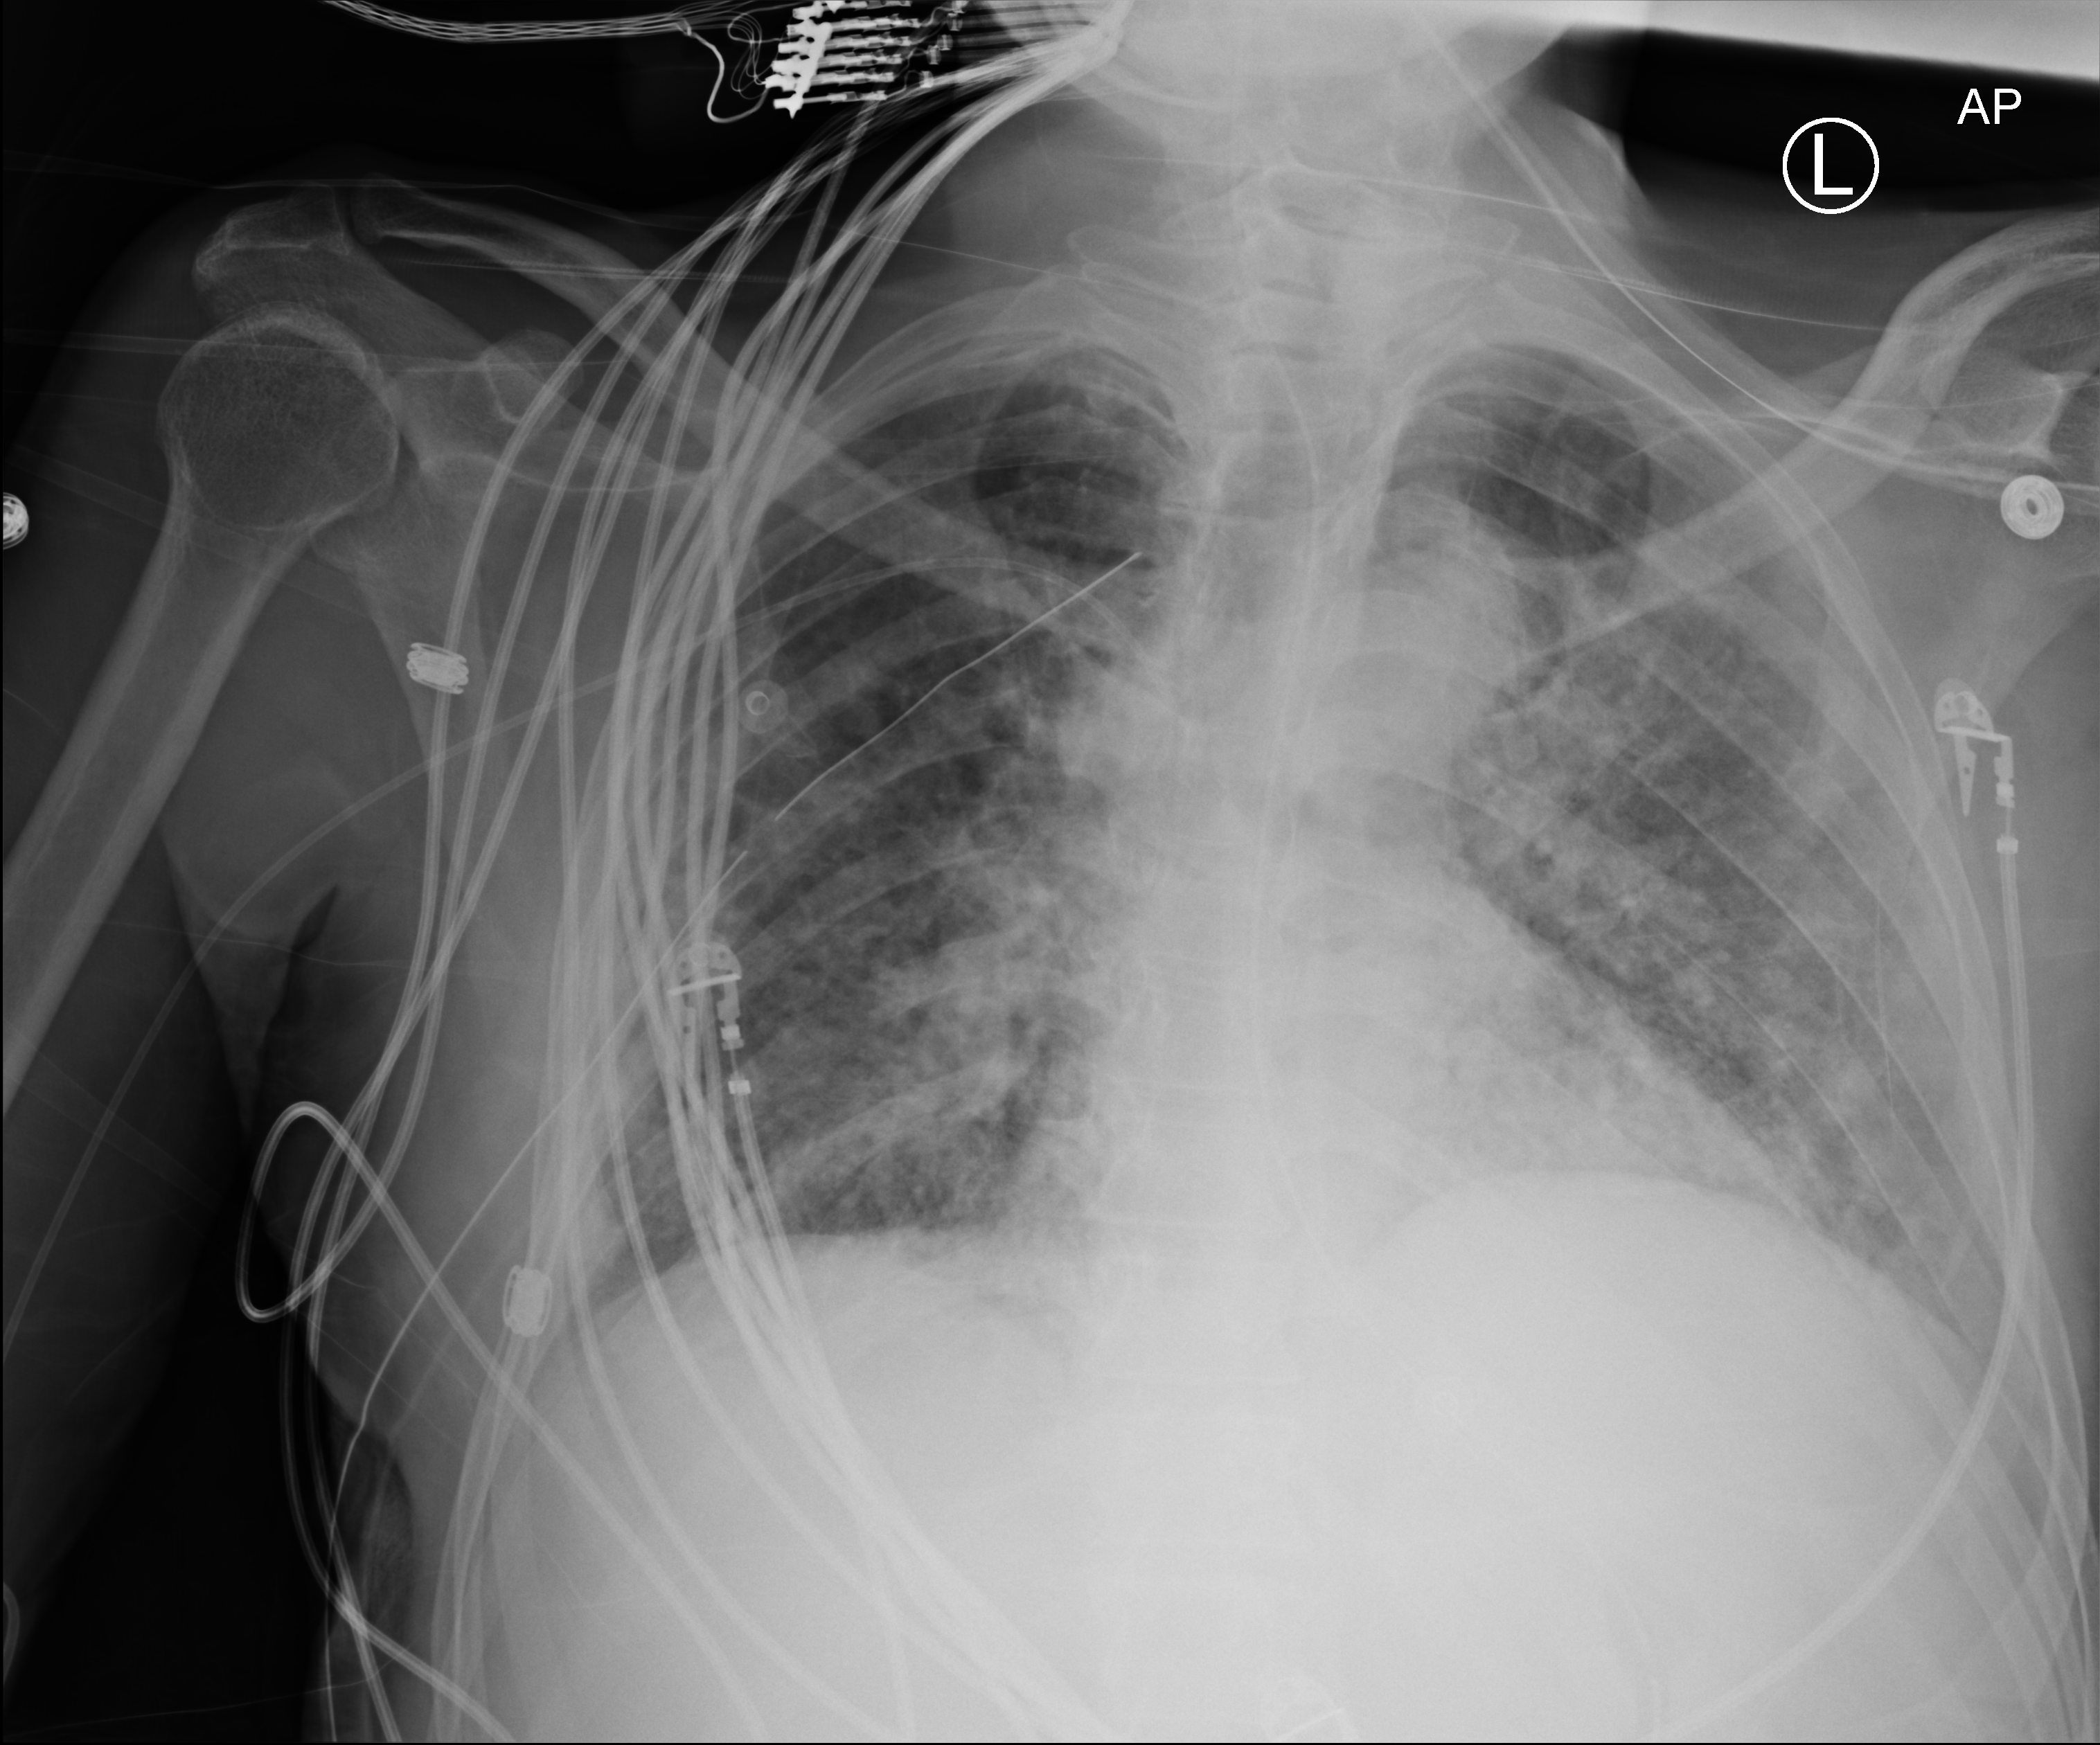
Bedside chest radiograph (computed radiography), anteroposterior (AP) projection. Patient hospitalised with COVID-19; male, aged 18–59 years.
Hospital-stay facts (about this admission, not read from this image; timing relative to this image not recorded): admitted to intensive care during this hospital stay: yes; length of hospital stay: 41 days.